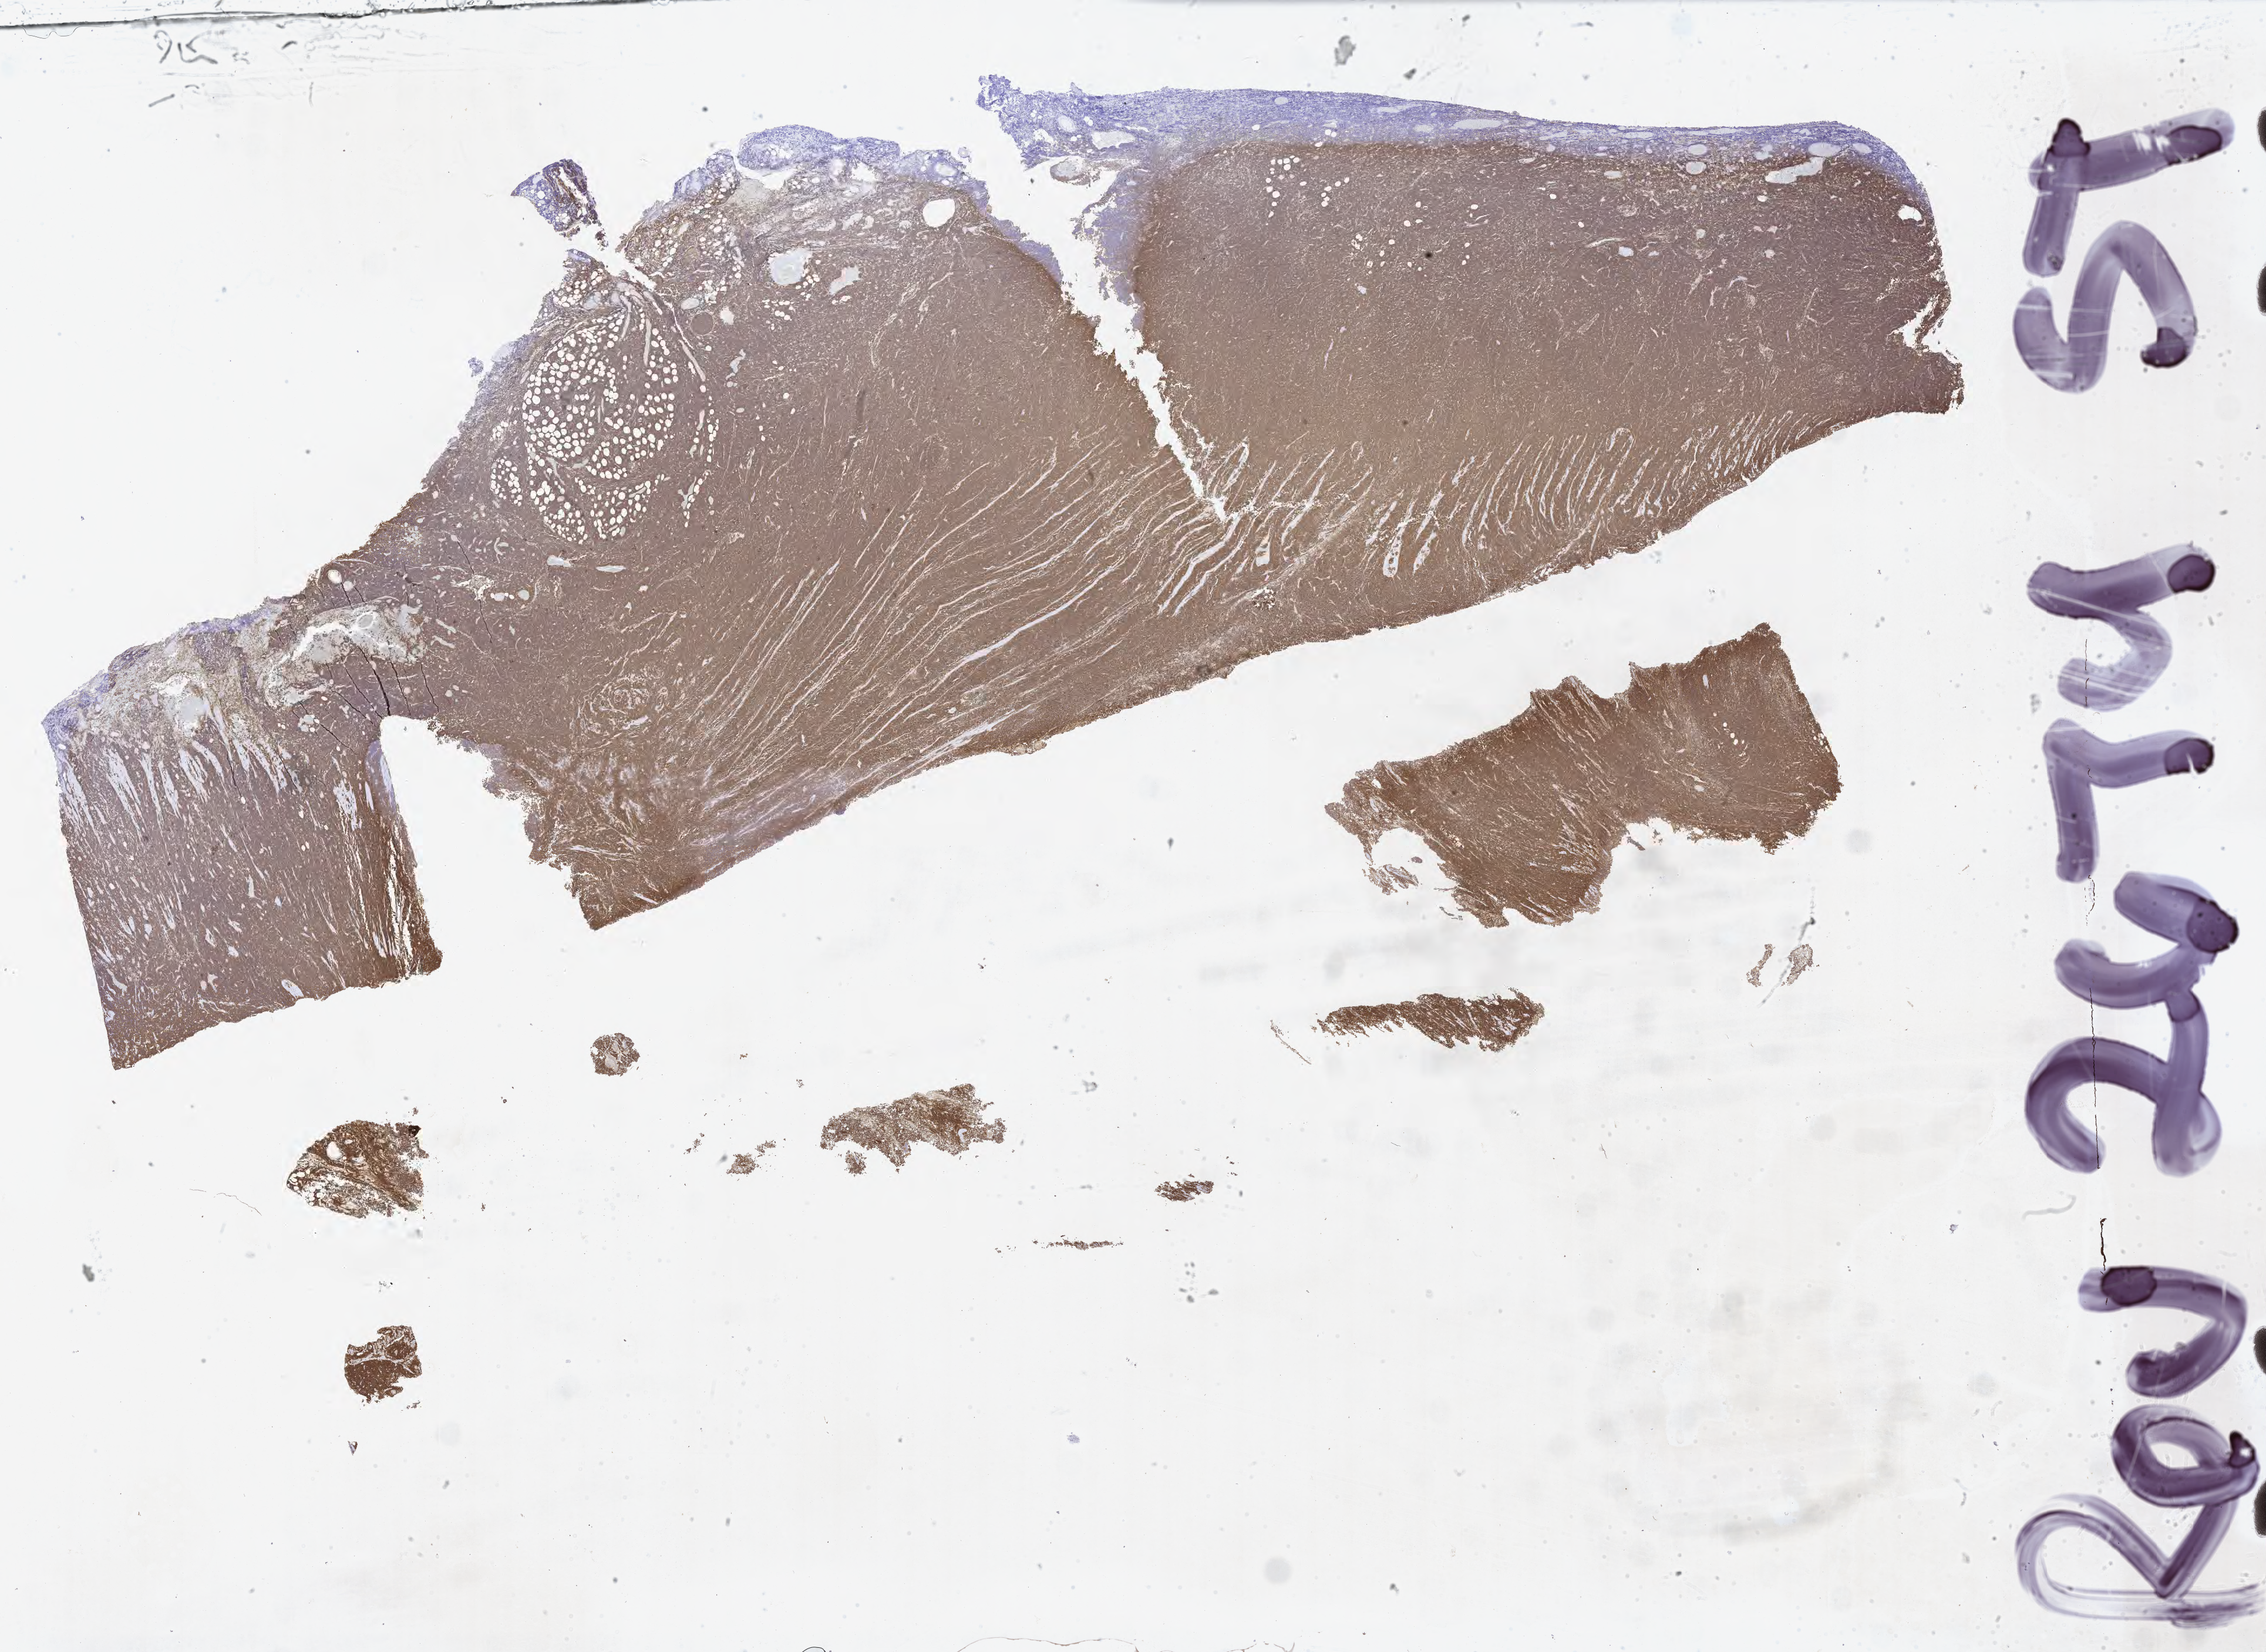
IHC for CD20, whole-slide image, shown as a low-resolution overview of the whole scanned area (about 31.2 x 22.7 mm); tumor tissue. Patient: male, 56 years old.
Histologic diagnosis: Burkitt lymphoma, NOS.